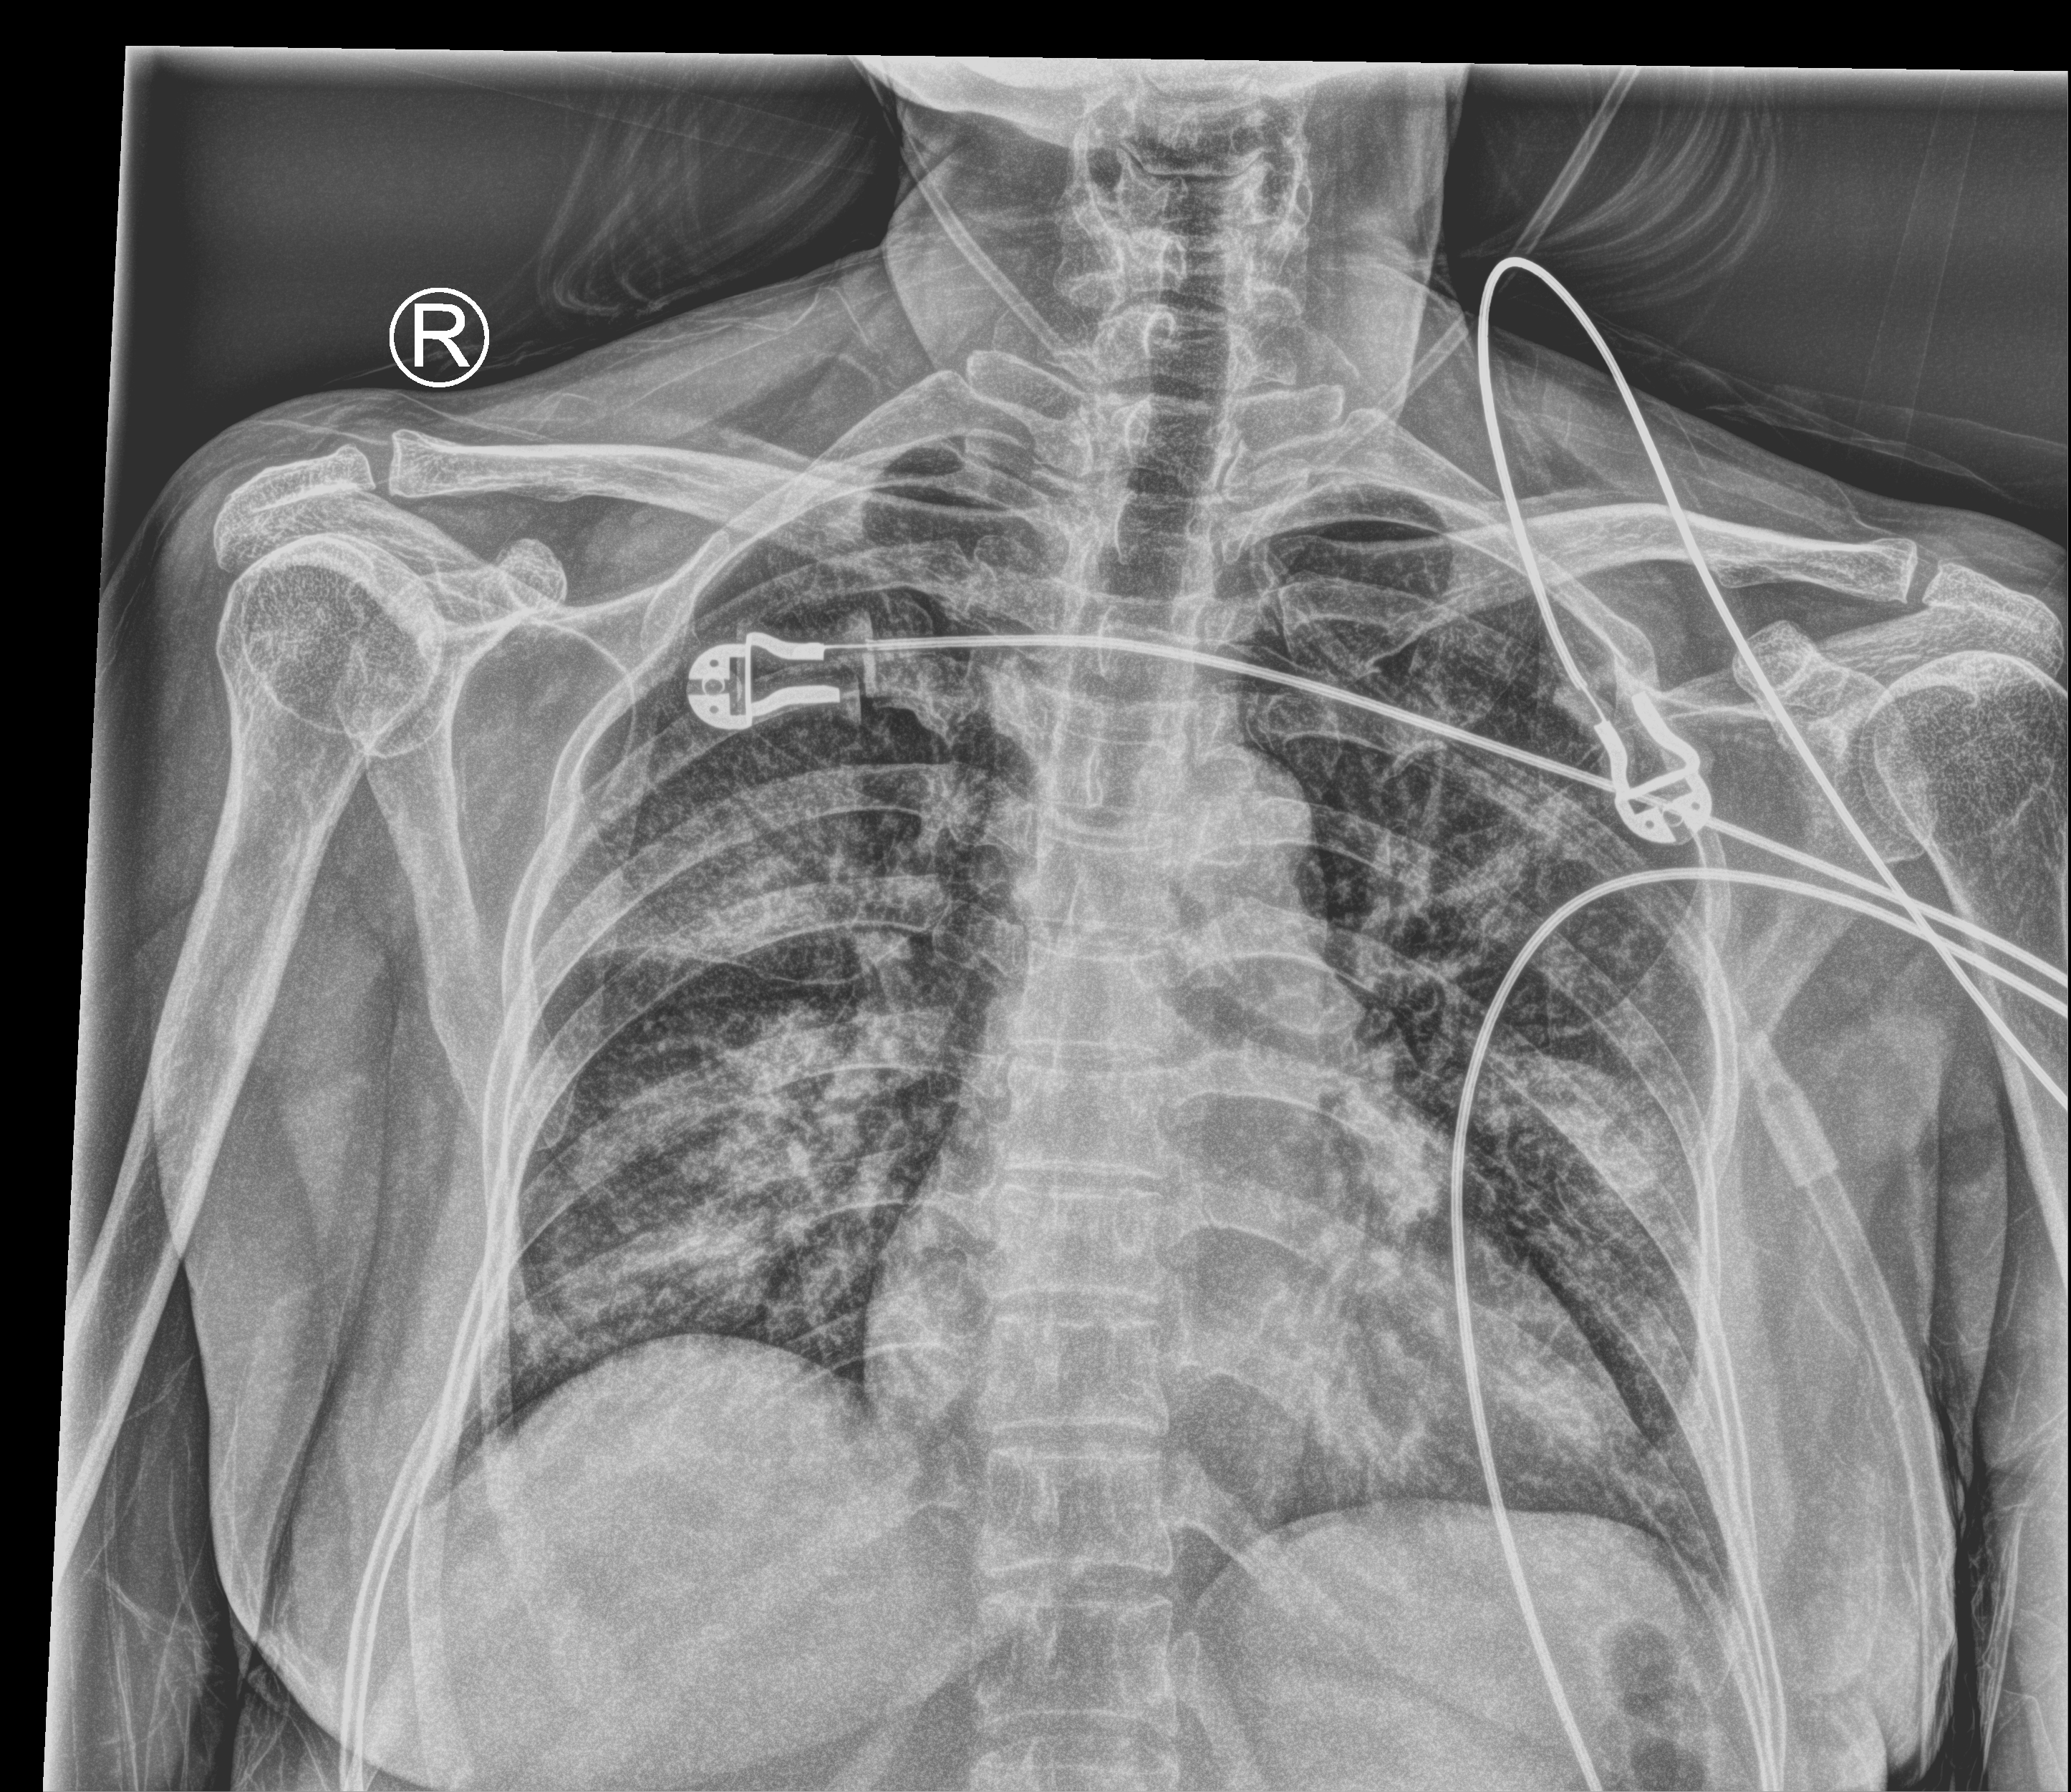
Portable chest radiograph, anteroposterior (AP) projection. Patient hospitalised with COVID-19; female, aged 60–74 years.
From the hospital-stay record, not from the radiograph (when in the stay this image was taken is not recorded):
- length of hospital stay: 17 days